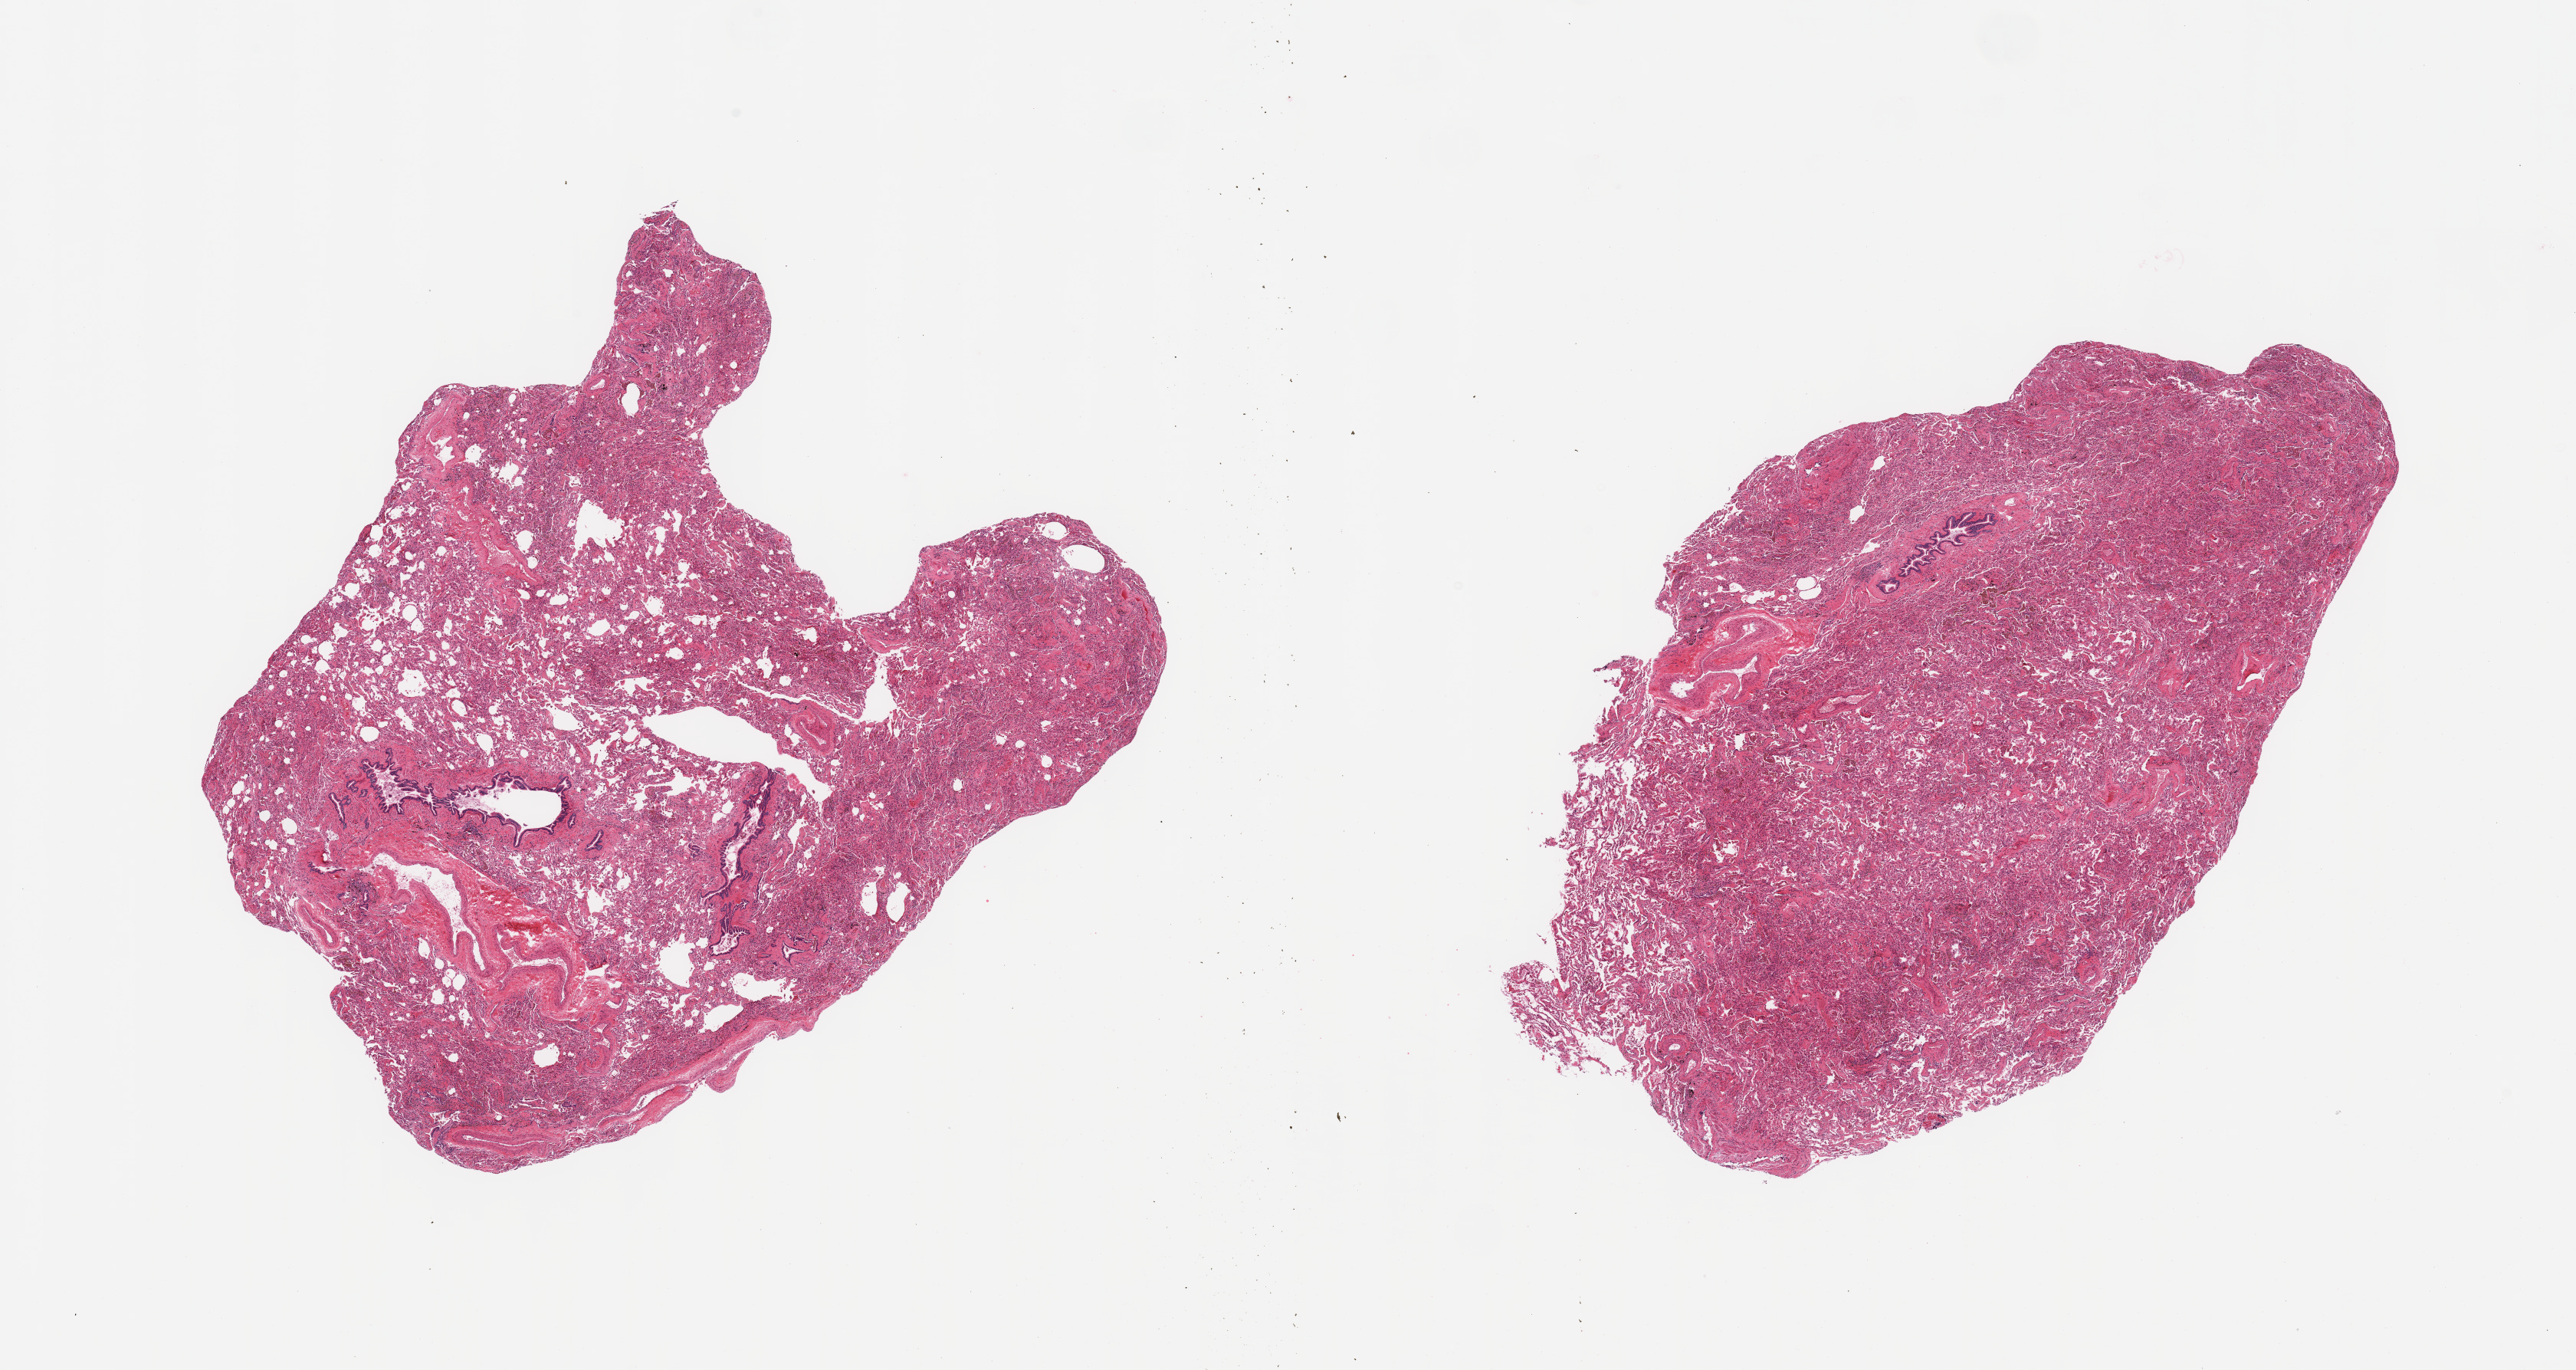
Haematoxylin and eosin whole-slide image, shown as a low-resolution overview of the whole scanned area (about 26.6 x 14.1 mm); PAXgene-fixed paraffin-embedded (PFPE) section; target tissue: lung; donor tissue sample.
Reviewer comment on this tissue sample: 2 pieces; some fibrosis and numerous pigmented macrophages, includes larger vessels/bronchi.